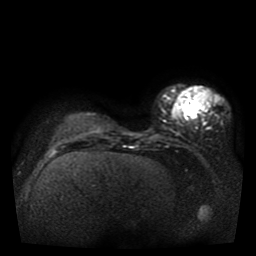
Breast MRI, one axial slice; position 11 of 41 along the scan axis; diffusion-weighted series; image 2 of 4 stored at this slice position (different b-values; order by instance number); 1.5 T; 256 × 256 image matrix, field of view 330 × 330 mm. Female patient.
Annotated regions visible in this slice (outlined manually by an expert reader):
- tumour on diffusion-weighted imaging: box from (x=186, y=110) to (x=197, y=119) px